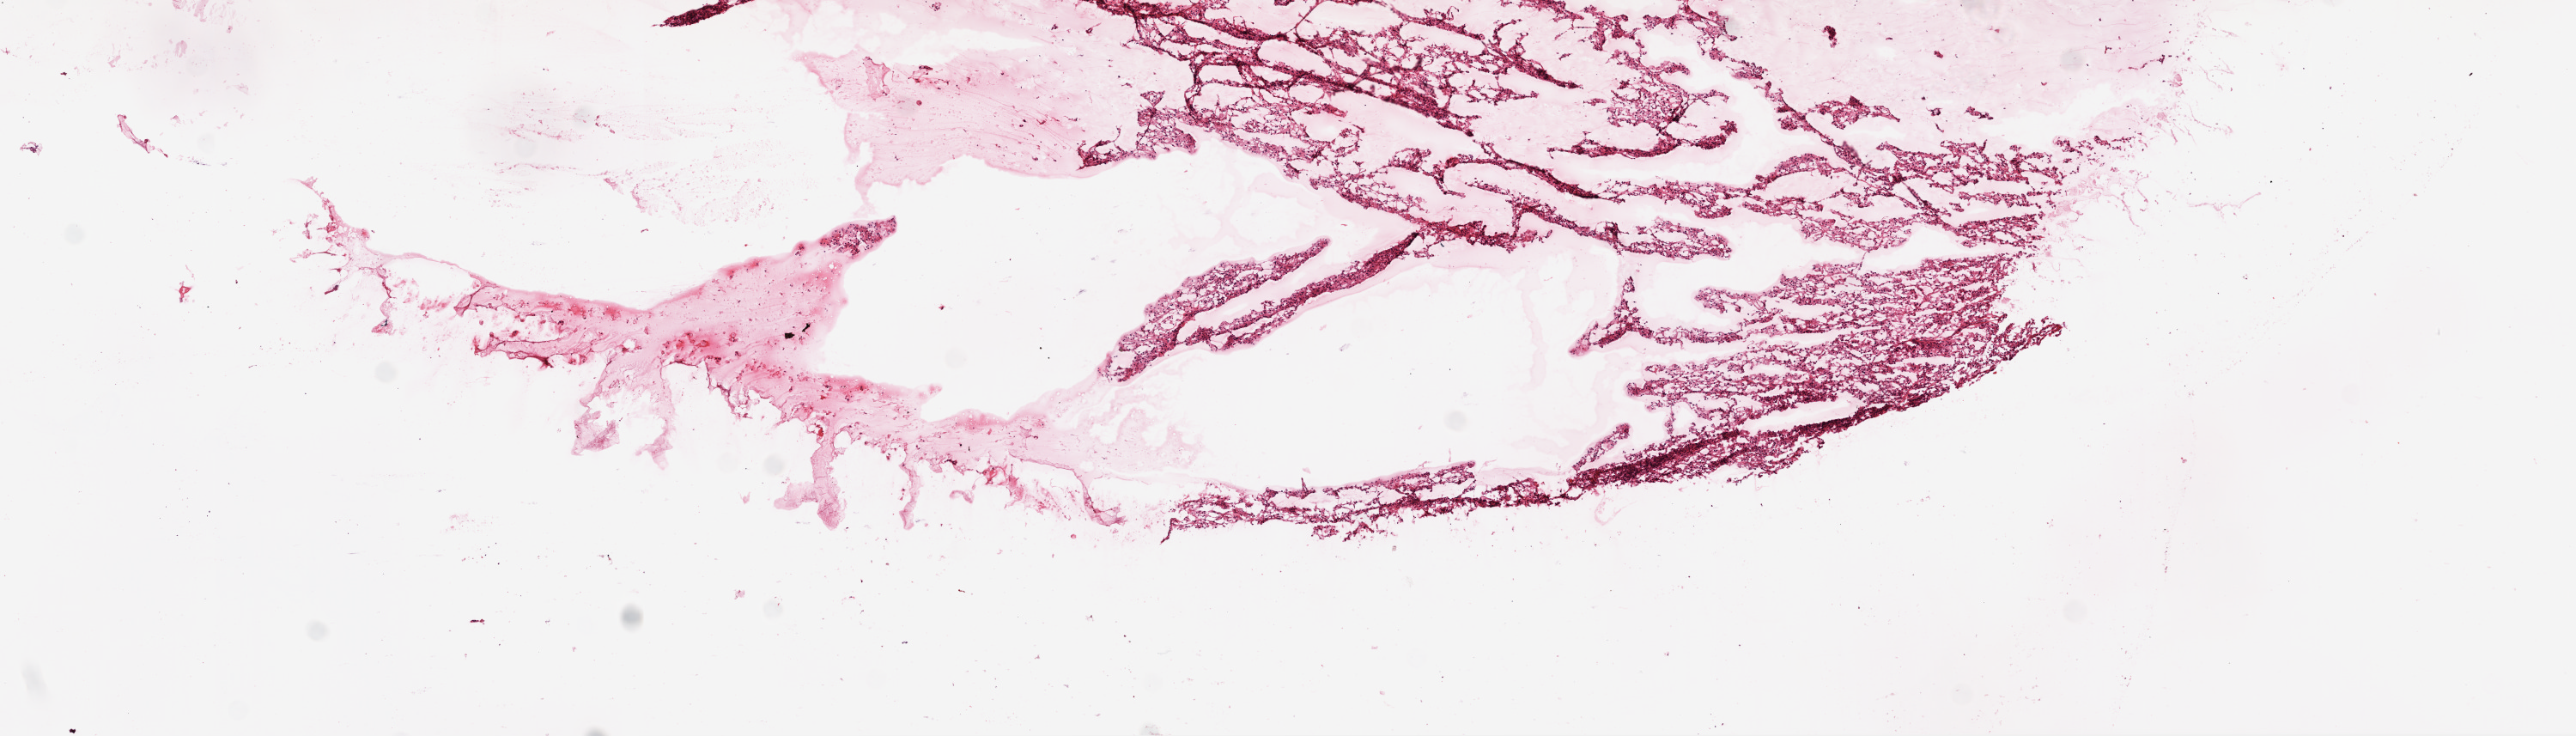
Whole-slide histology image, Hematoxylin and eosin (H&E) stained, whole scanned area (about 12.0 x 3.4 mm, acquisition: 20x scan) shown as a low-resolution overview; frozen section; kidney, primary tumour sample. Patient: male, age at initial diagnosis 62 years. Histologic grade: G2 (moderately differentiated). Composition of this section per pathologist review: tumour cells 95%, tumour nuclei 85%, normal cells 0%, stromal cells 5%, necrosis 0%.
- histologic diagnosis: Clear cell adenocarcinoma, NOS
- AJCC pathologic stage: IV
- laterality: left